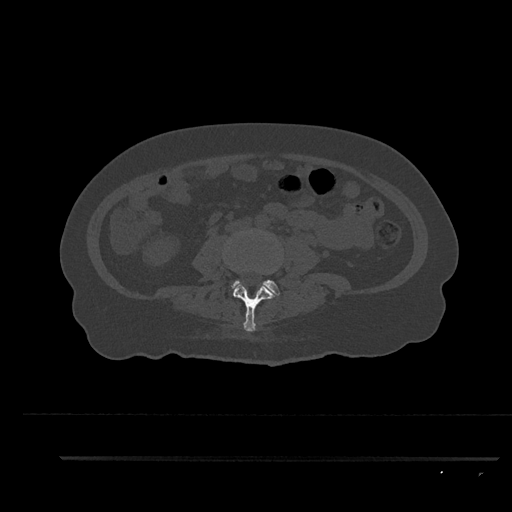
CT including the spine, one axial slice; position 59 of 797 along the scan axis; reconstruction kernel Br40s/3; 120 kVp; bone window (W 1800 / L 400 HU); 0.5 mm slice thickness; 512 × 512 image matrix, field of view 408 × 408 mm. Patient: female, 44 years. From the clinical record (not read from this slice): primary cancer: renal; vertebrae with lytic lesions (as recorded): L1.
Structures marked on this image (semi-automatically segmented with operator editing):
- L3 vertebra: box from (x=233, y=282) to (x=279, y=331) px
- L4 vertebra: (x=231, y=280)–(x=281, y=295)